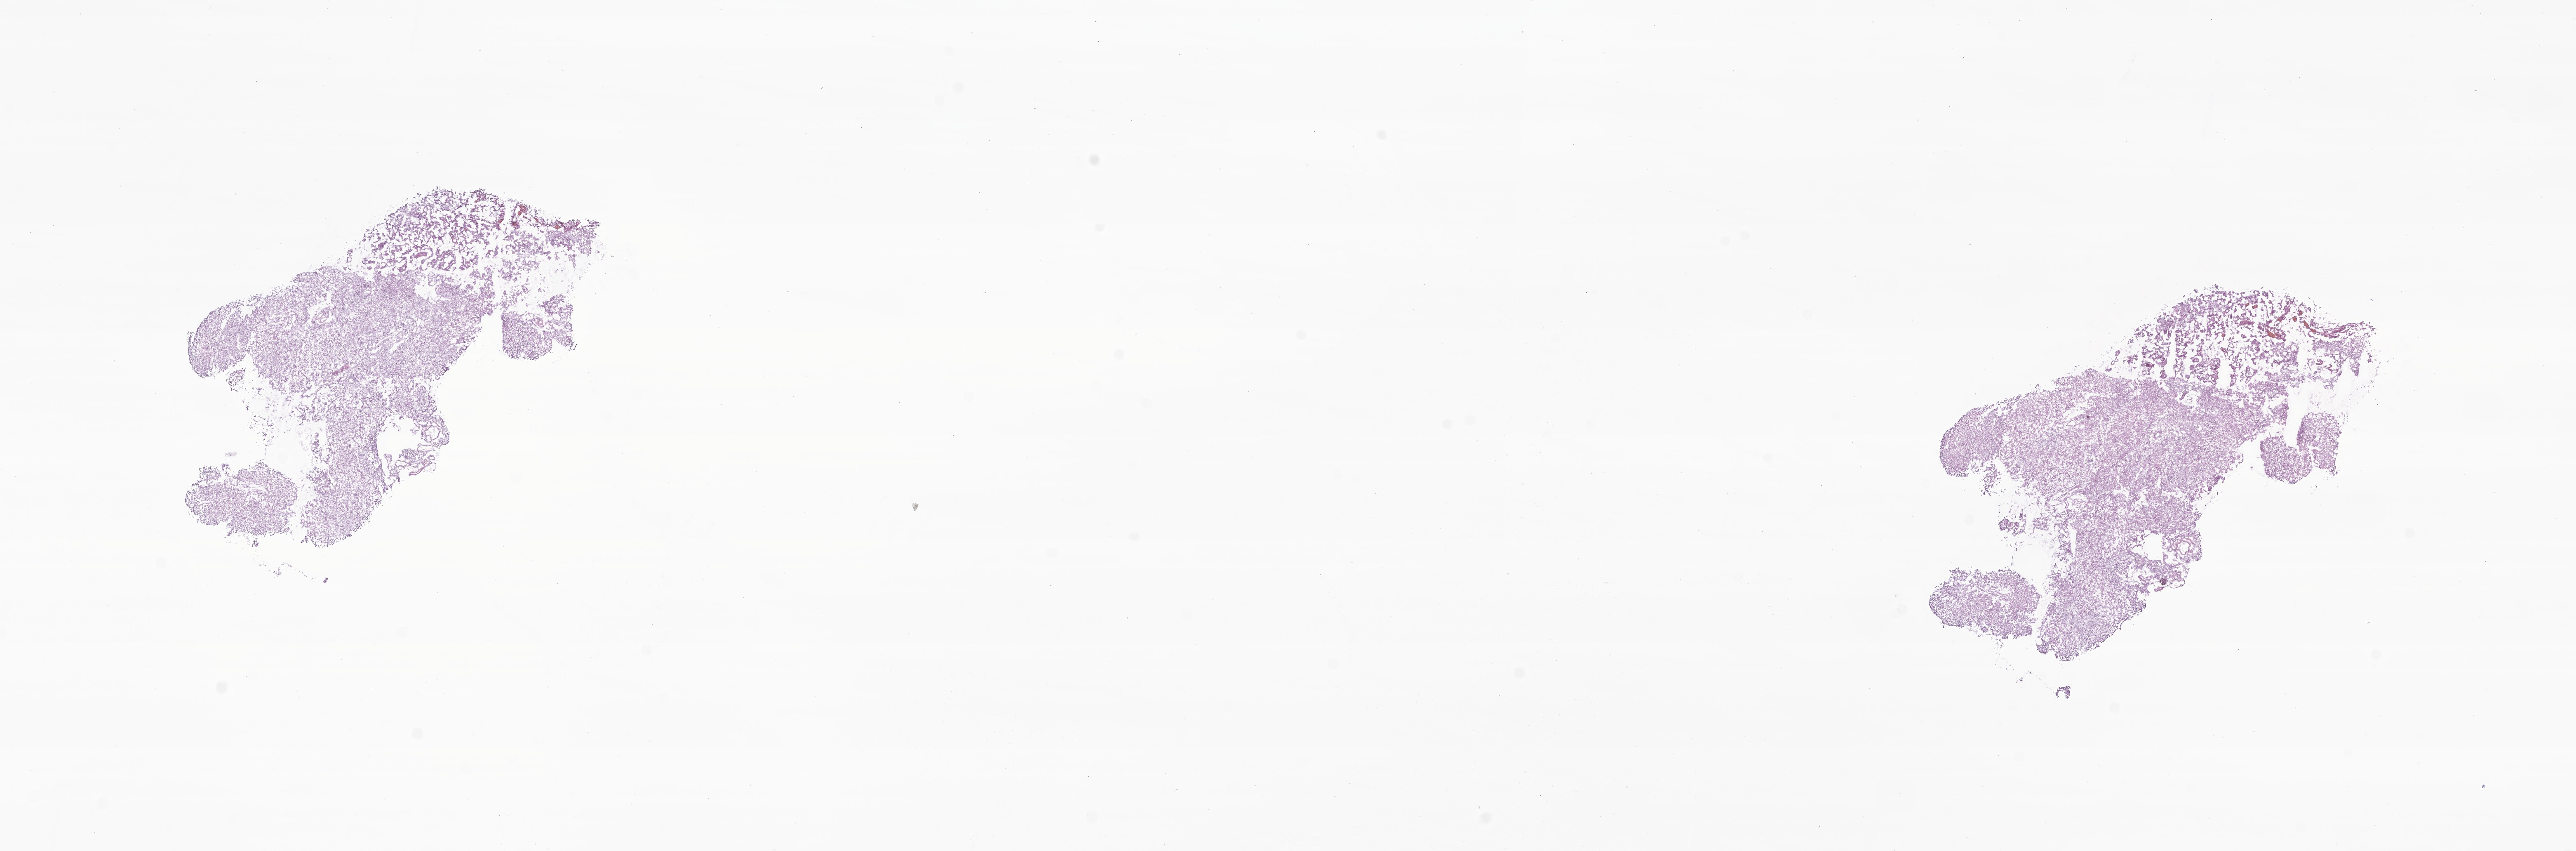
Digitized H&E-stained section of tumor tissue from the brain — a low-resolution overview of the entire scanned area, about 26.3 x 8.7 mm. Frozen section (OCT-embedded). Patient female; age 143 months (11 years 11 months).
Recorded diagnosis: Meningothelial meningioma.